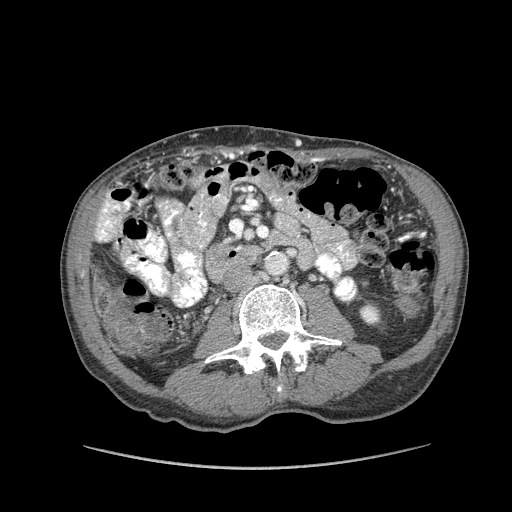
Contrast-enhanced abdominal CT (liver protocol), one axial slice; slice 5 of 162 in the series (ordered by position); 100 kVp; soft-tissue window (W 400 / L 40 HU); 2.5 mm slice thickness; 512 × 512 image matrix, field of view 400 × 400 mm. Case-level facts recorded for this patient, not image findings: diagnosis: hepatocellular carcinoma (patient treated with transarterial chemoembolisation; whether this scan precedes or follows treatment is not stated here); TNM stage (as recorded): Stage-IIIA; Child-Pugh class: A; tumour nodularity: multinodular.
Outlined on this slice (semi-automatic segmentation, software-assisted and operator-edited):
- liver parenchyma outside the tumour (the mass and vessels are separate outlines, so this box may not span the whole liver): box from (x=94, y=195) to (x=132, y=354) px
- liver vessels: (x=97, y=201)–(x=117, y=240)